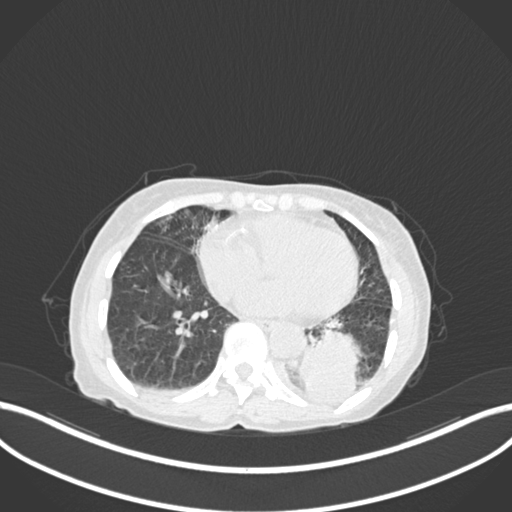
Chest CT, one axial slice; slice 43 of 233 in the series (ordered by position); reconstruction kernel B30f; lung window (W 1500 / L -600 HU); 1 mm slice thickness; 512 × 512 image matrix, field of view 400 × 400 mm. Patient: female, 78 years. From the clinical record (not read from this slice): clinical TNM (as recorded): T3 N0 M1.
Annotated regions visible in this slice (rectangle marked by the reading radiologist):
- lung tumour (recorded histology: squamous cell carcinoma): bounding box (x1, y1, x2, y2) in pixels: (300, 323, 361, 407)